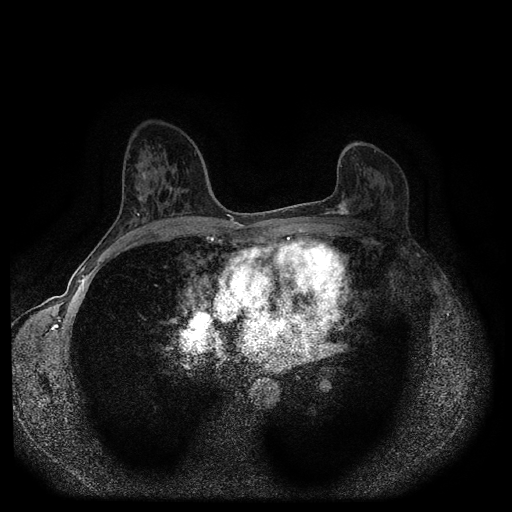
Breast MRI (dynamic contrast-enhanced, multi-phase), one axial slice; slice 55 of 116 in the series (ordered by position); dynamic contrast-enhanced series, time point 2 of 5 at this slice position (early post-contrast); 1.5 T; TE 2.6 ms, TR 5.4 ms; 512 × 512 image matrix. Female patient, age 57 years.
Annotated regions visible in this slice (semi-automatic segmentation, software-assisted and operator-edited):
- breast lesion (labelled 'tumour' in the annotation; benign lesions carry a separate 'benign' label): bounding box (x1, y1, x2, y2) in pixels: (324, 193, 350, 218)